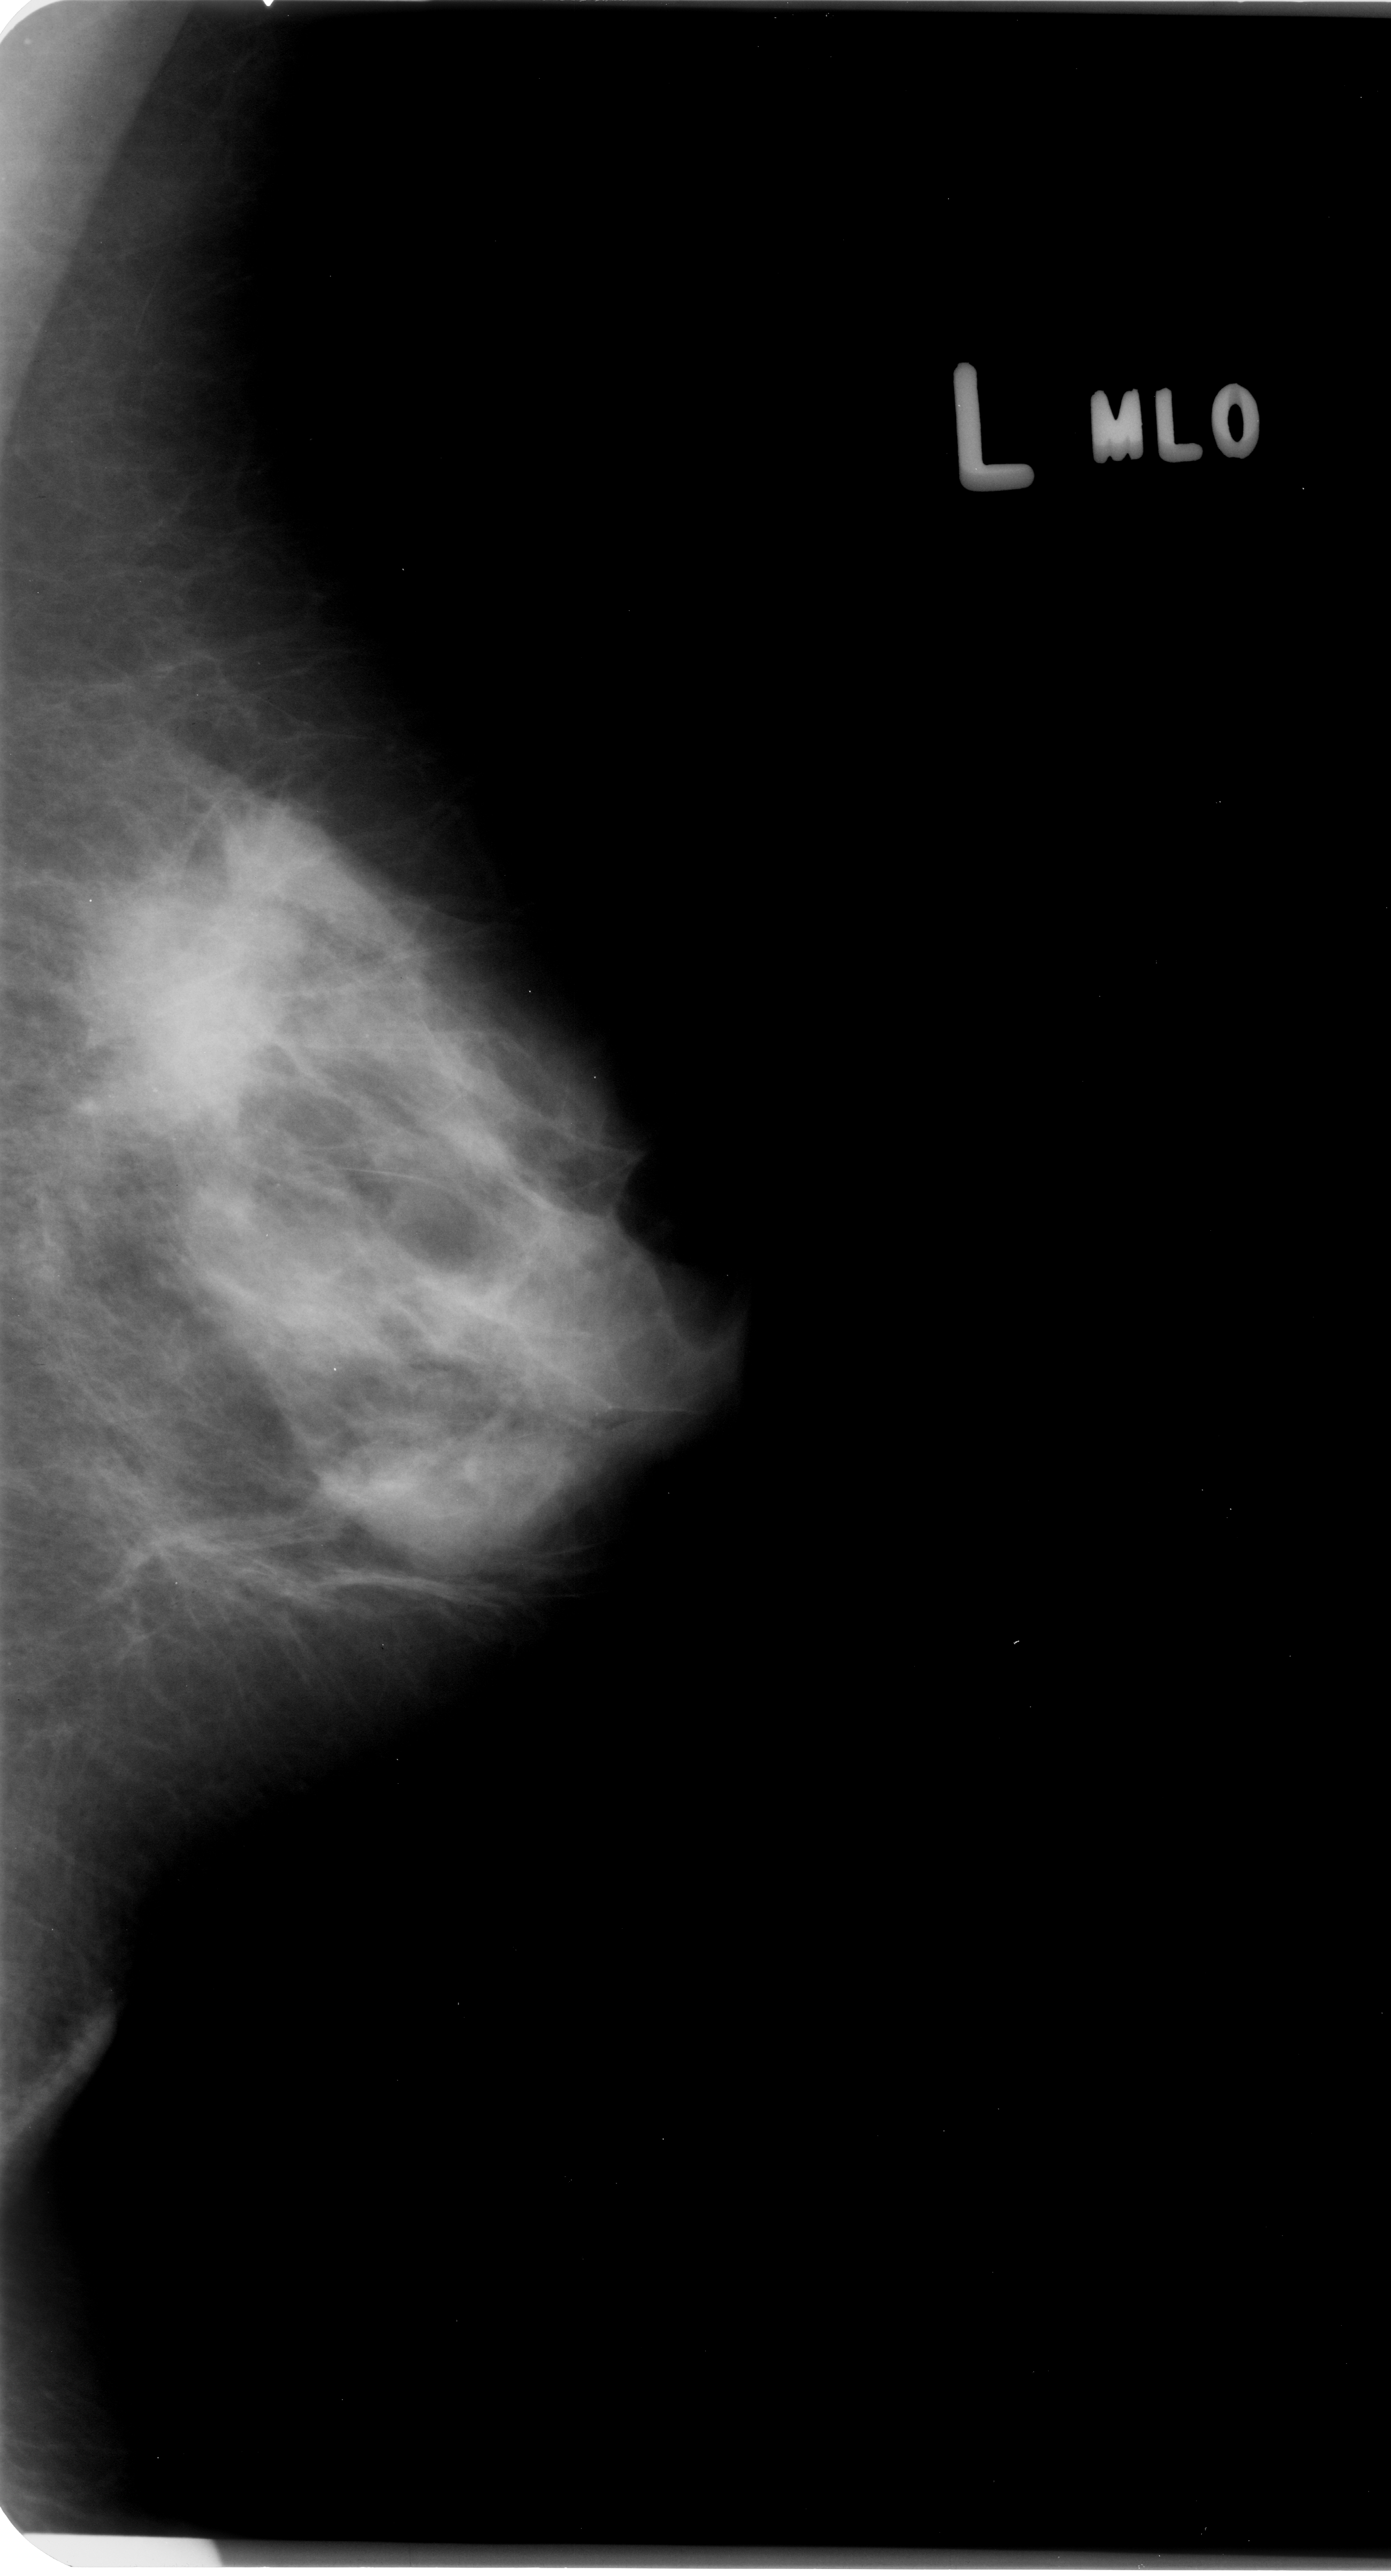
Scanned film-screen mammogram; left breast; mediolateral oblique (MLO) view; breast composition: heterogeneously dense (BI-RADS density category 3 of 4); 1391 × 2576 image matrix.
Expert-marked regions of interest on this film, with their recorded descriptors:
- mass, shape irregular / architectural distortion, margins obscured / spiculated; BI-RADS assessment category 4; subtlety rating 4 on a 1 (subtle) to 5 (obvious) scale; pathology (as recorded): malignant: box from (x=117, y=949) to (x=290, y=1148) px